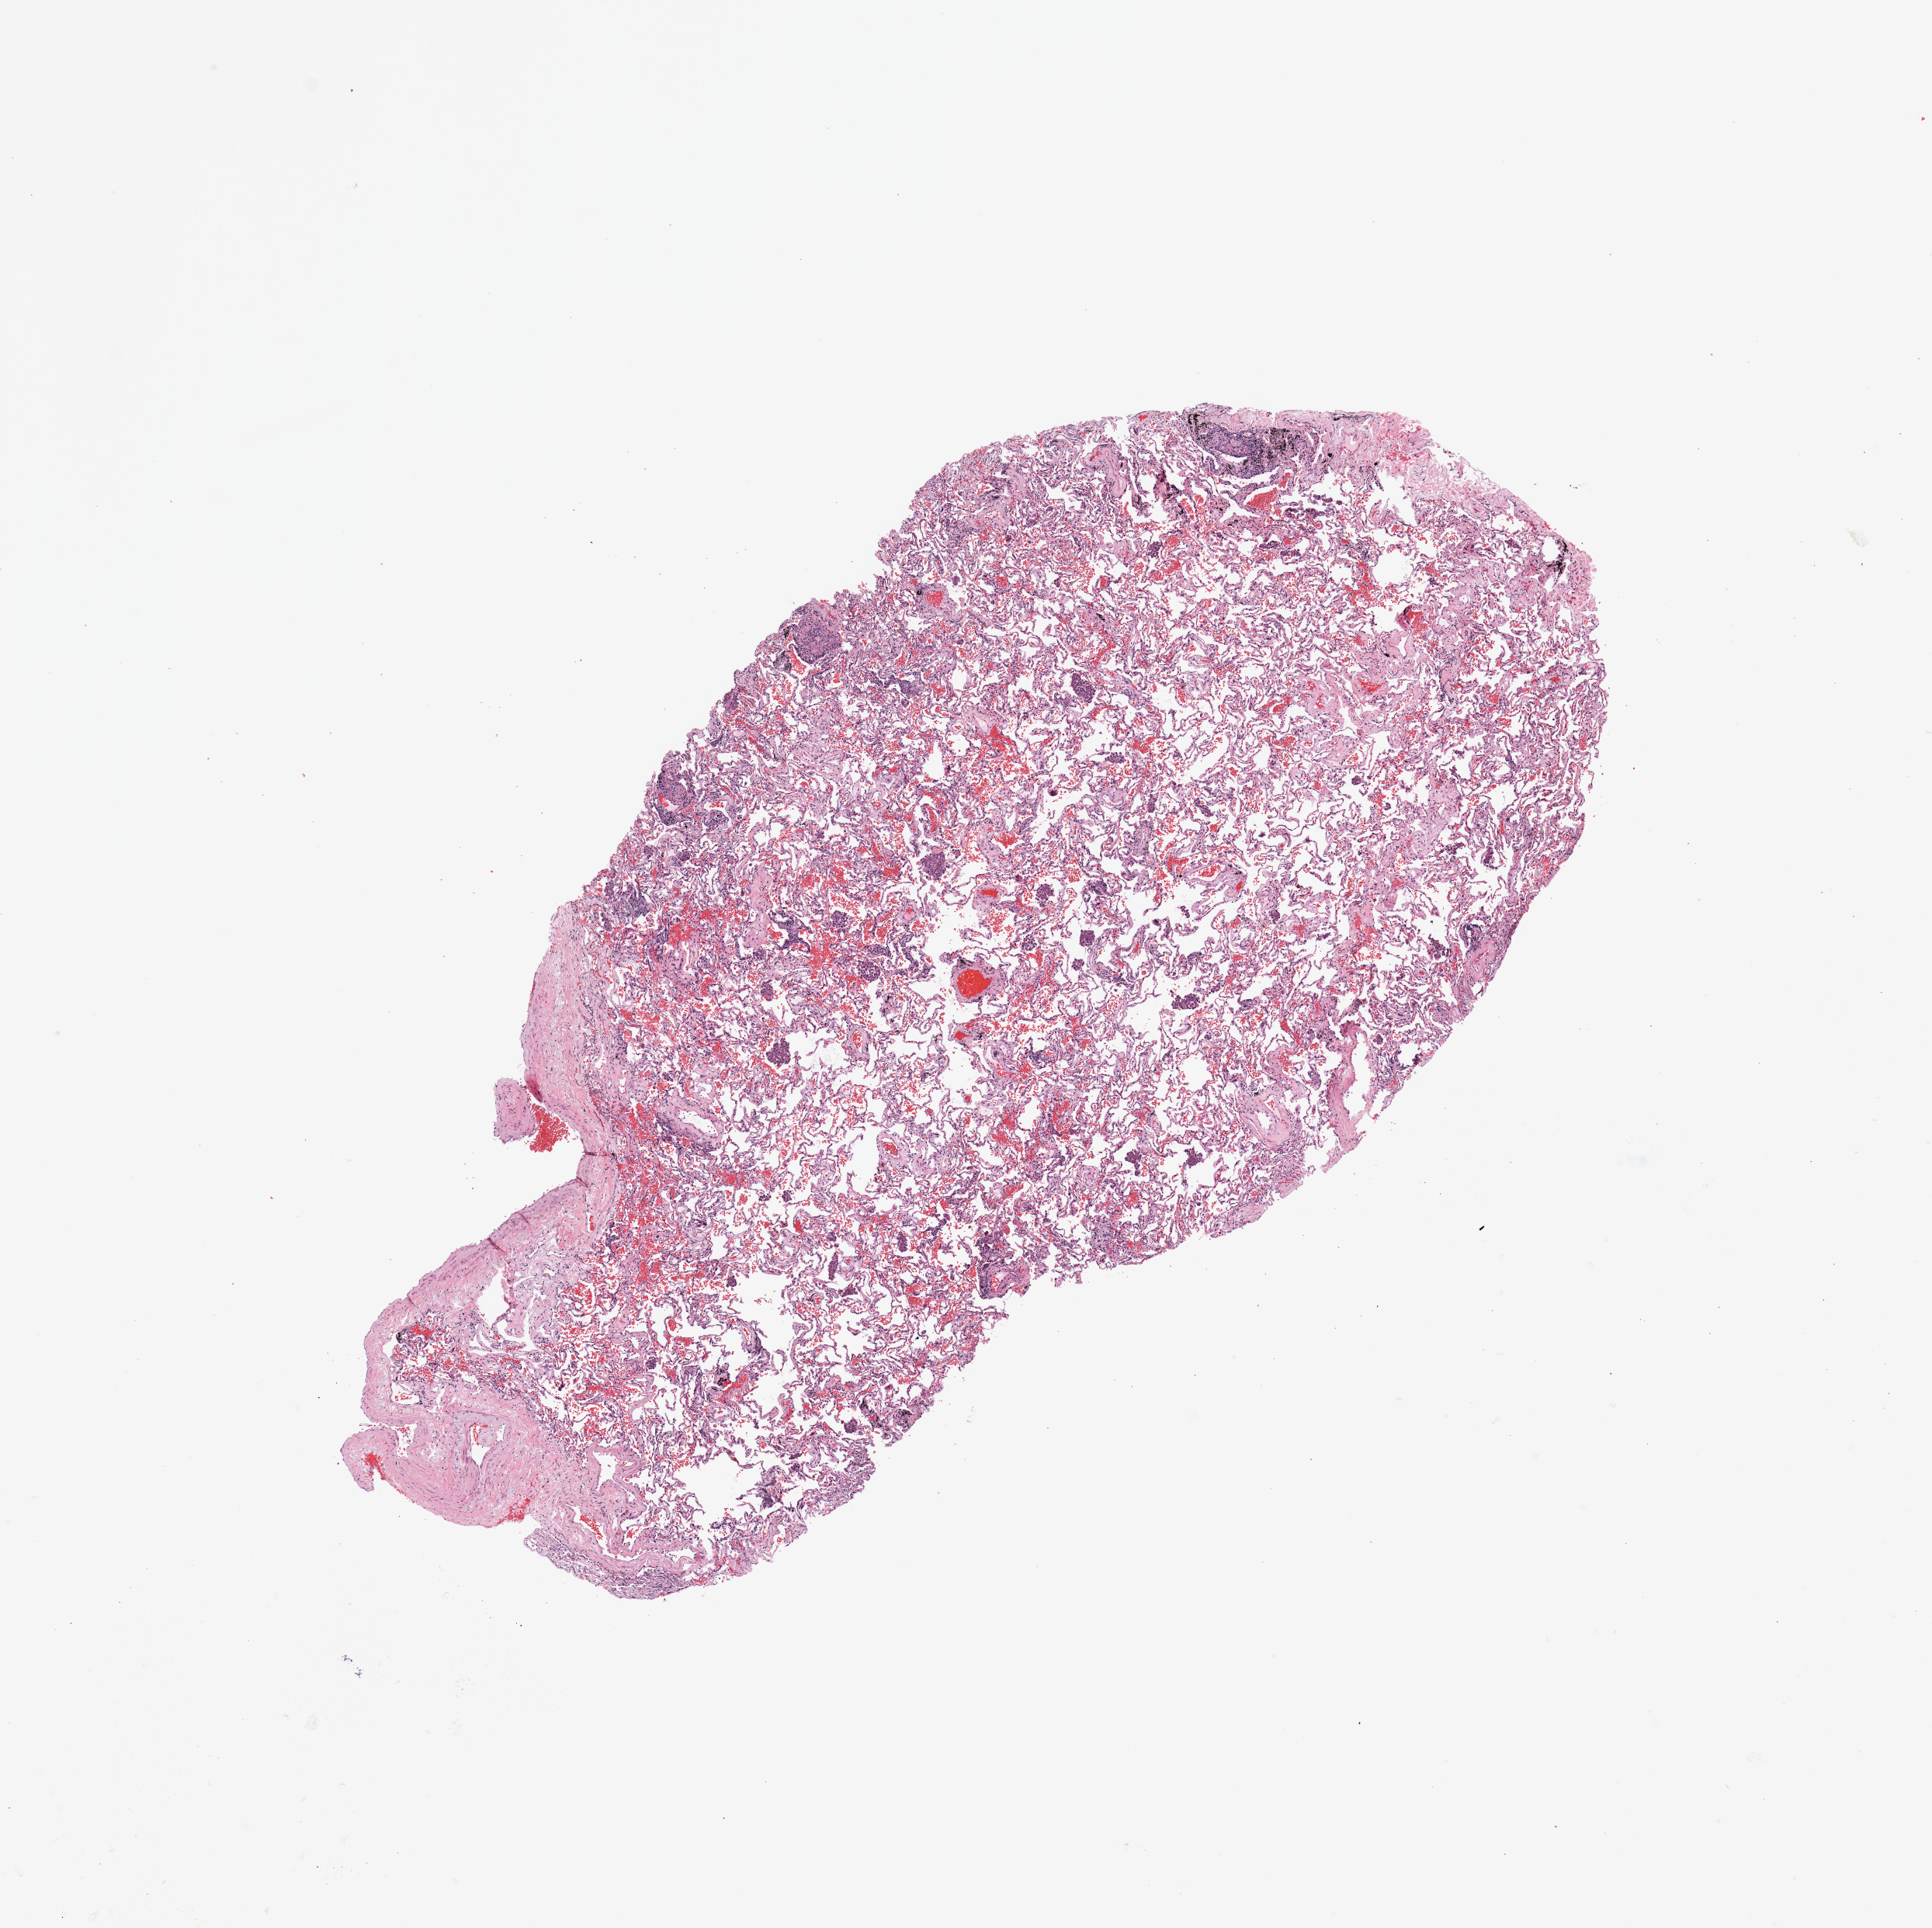
Digitized H&E-stained tissue section (whole slide), whole scanned area (about 9.8 x 9.8 mm) shown as a low-resolution overview; normal (non-tumour) tissue sample, lung. 78-year-old female patient.
* this section: normal (non-tumour) tissue from the same patient
* patient diagnosis: Adenocarcinoma, NOS